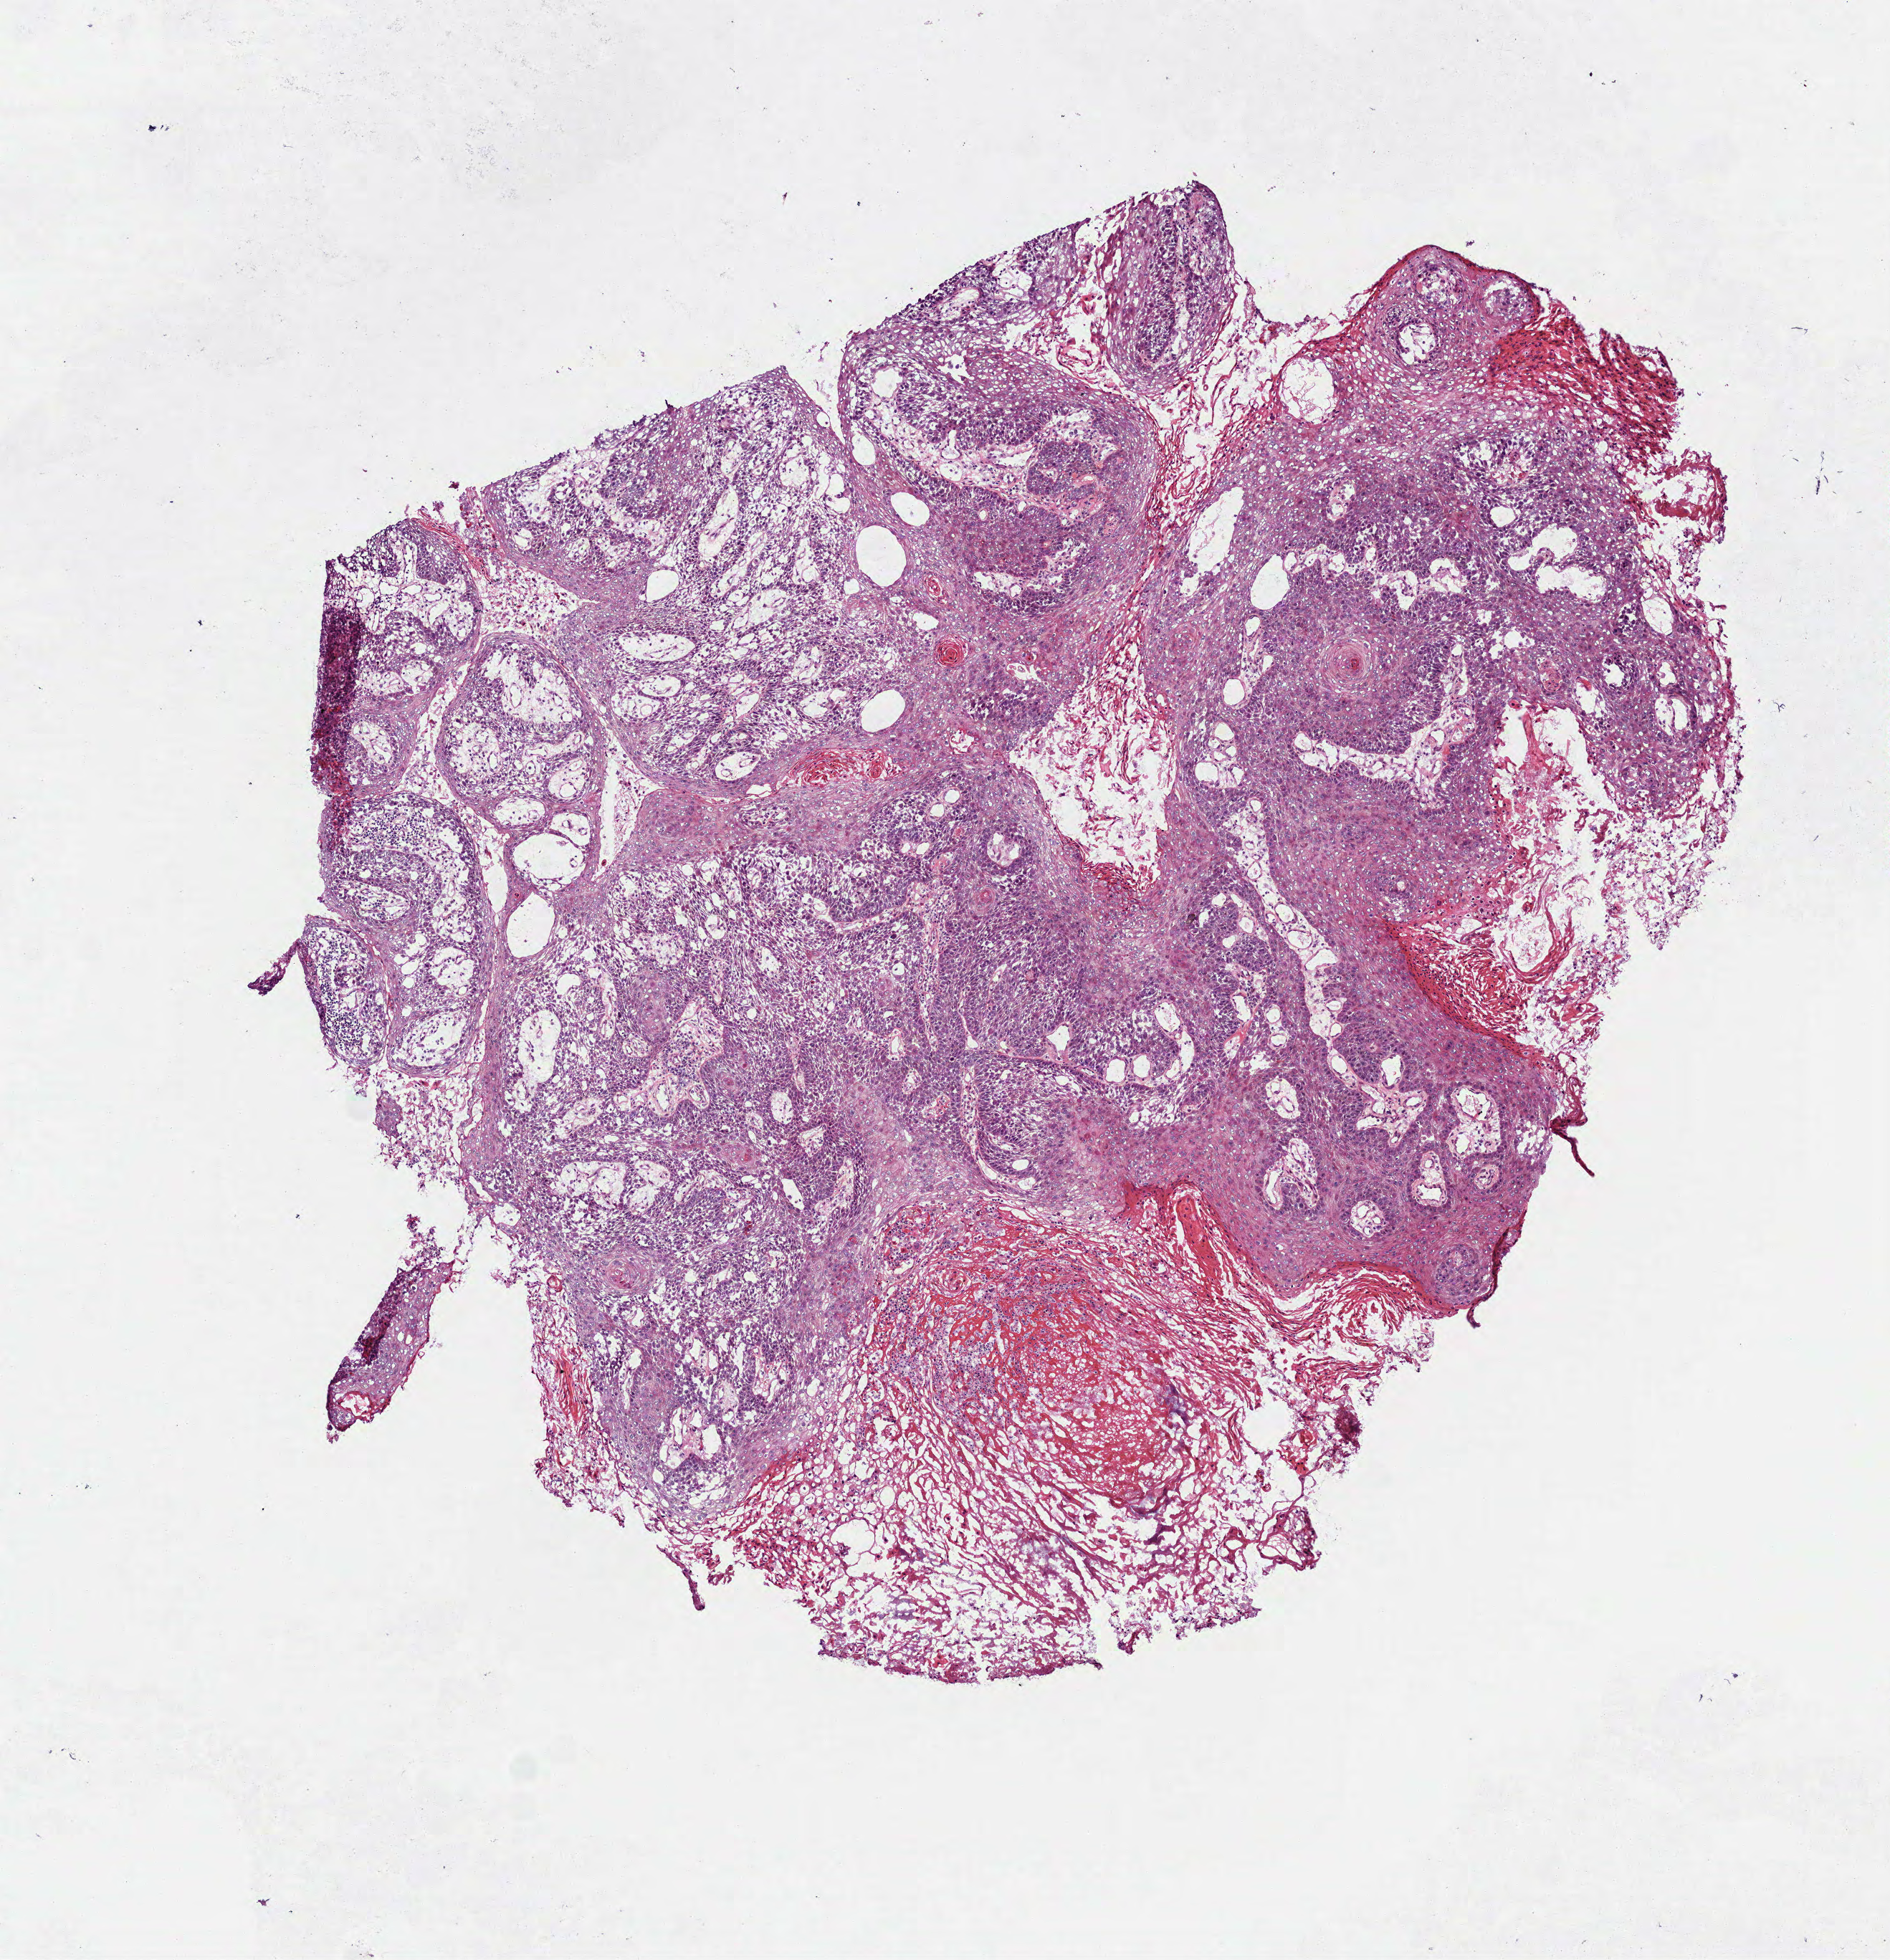
H&E-stained whole-slide image, whole scanned area (about 5.3 x 5.5 mm, acquisition: 40x scan) shown as a low-resolution overview; frozen section from the top of the tissue portion; primary tumour sample from the head and neck. Male patient; age at initial diagnosis 53 years. Histologic grade: G2 (moderately differentiated). Composition of this section per pathologist review: tumour cells 99%, tumour nuclei 80%, normal cells 0%, stromal cells 0%, necrosis 1%. Infiltration values recorded for this section: lymphocyte infiltration 7%, monocyte infiltration 0%, neutrophil infiltration 10%.
* pathologic diagnosis: Squamous cell carcinoma, NOS (floor of mouth, NOS)
* AJCC pathologic stage: III (7th edition)